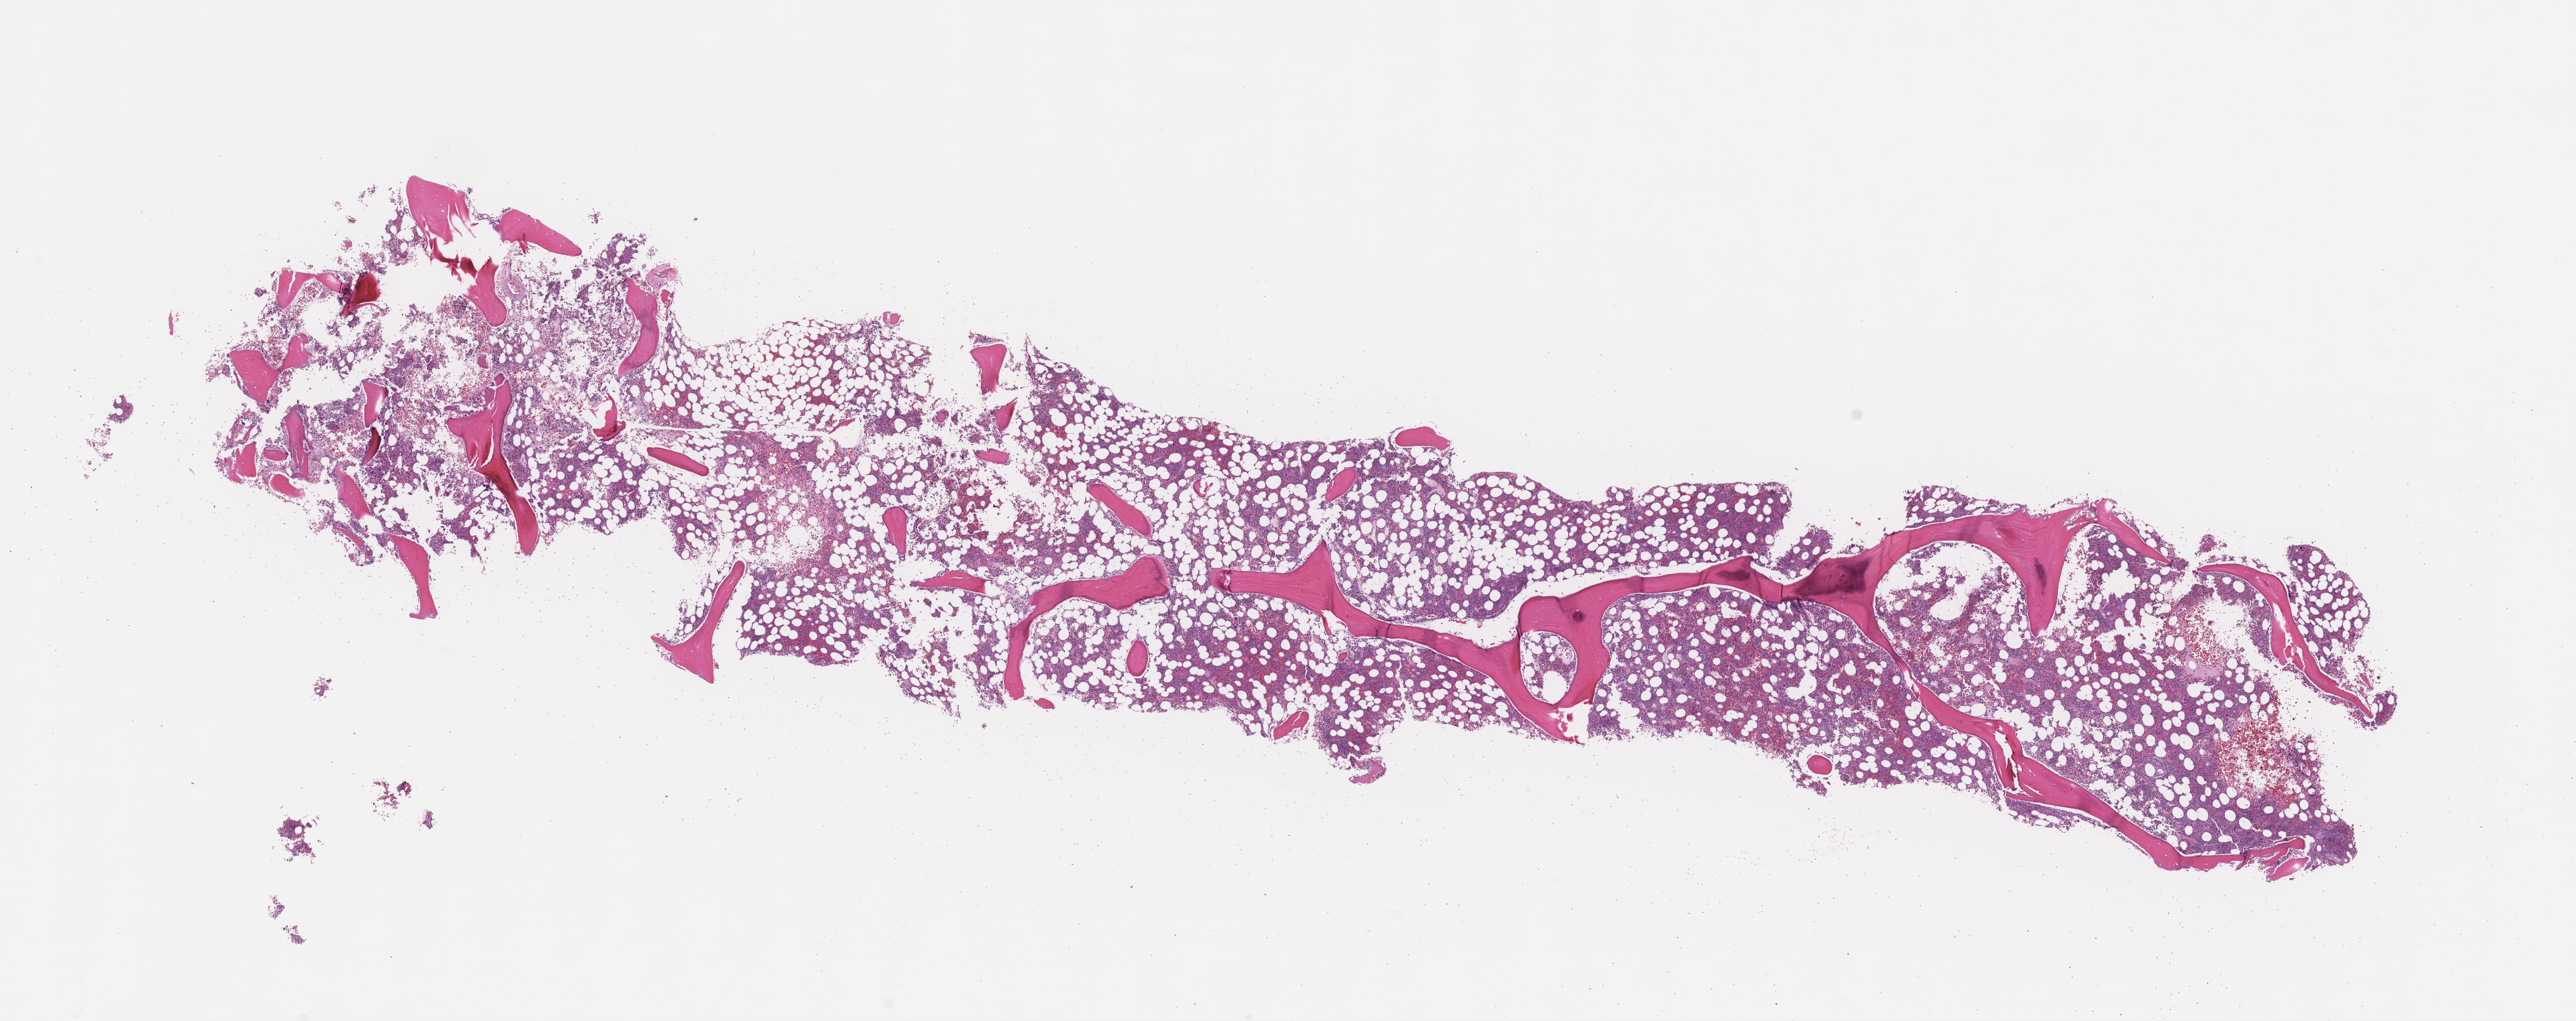
Digitized haematoxylin and eosin-stained section, low-resolution overview of the scanned area, about 15.6 x 6.2 mm. FFPE section. Tissue site: bone marrow. Archival tissue. Patient sex: male.
* this section: primary tumour tissue
* diagnosis: Plasma Cell Myeloma